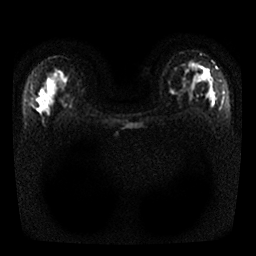
Breast MRI, one axial slice. Position 19 of 25 along the scan axis. Diffusion-weighted series; image 2 of 4 stored at this slice position (different b-values; order by instance number). 1.5 T. 256 × 256 image matrix. Female patient.
Annotated regions visible in this slice (expert manual segmentation):
- tumour on diffusion-weighted imaging: bounding box <197,63,214,82> (left, top, right, bottom; pixels)